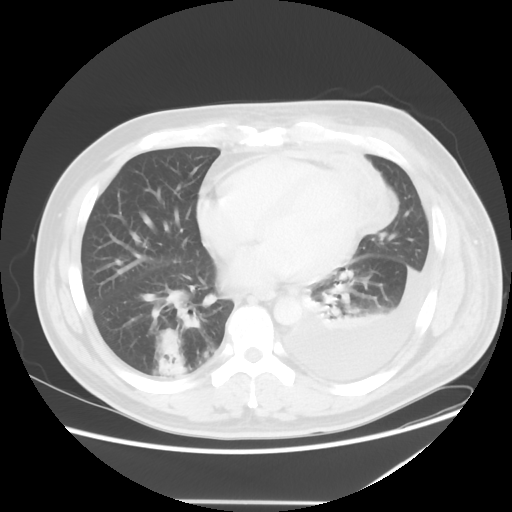
Chest CT, one axial slice; slice 19 of 52 in the series (ordered by position); reconstruction kernel STANDARD; lung window (W 1500 / L -600 HU); 5 mm slice thickness; 512 × 512 image matrix. Male patient, age 42 years. Case-level facts recorded for this patient, not image findings: clinical TNM (as recorded): T2 N1 M1.
Outlined on this slice (bounding box drawn by a radiologist):
- lung tumour (recorded histology: adenocarcinoma): box from (x=145, y=324) to (x=180, y=367) px